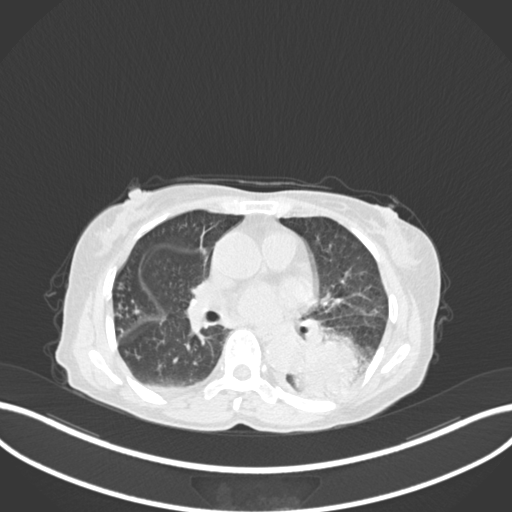
Chest CT, one axial slice; position 83 of 233 along the scan axis; 120 kVp; lung window (W 1500 / L -600 HU); 1 mm slice thickness; 512 × 512 image matrix, field of view 400 × 400 mm. Female patient, age 78 years. Case-level facts recorded for this patient, not image findings: clinical TNM (as recorded): T3 N0 M1.
Structures marked on this image (rectangle marked by the reading radiologist):
- lung tumour (recorded histology: squamous cell carcinoma): bounding box [x1, y1, x2, y2] px = [289, 330, 369, 402]